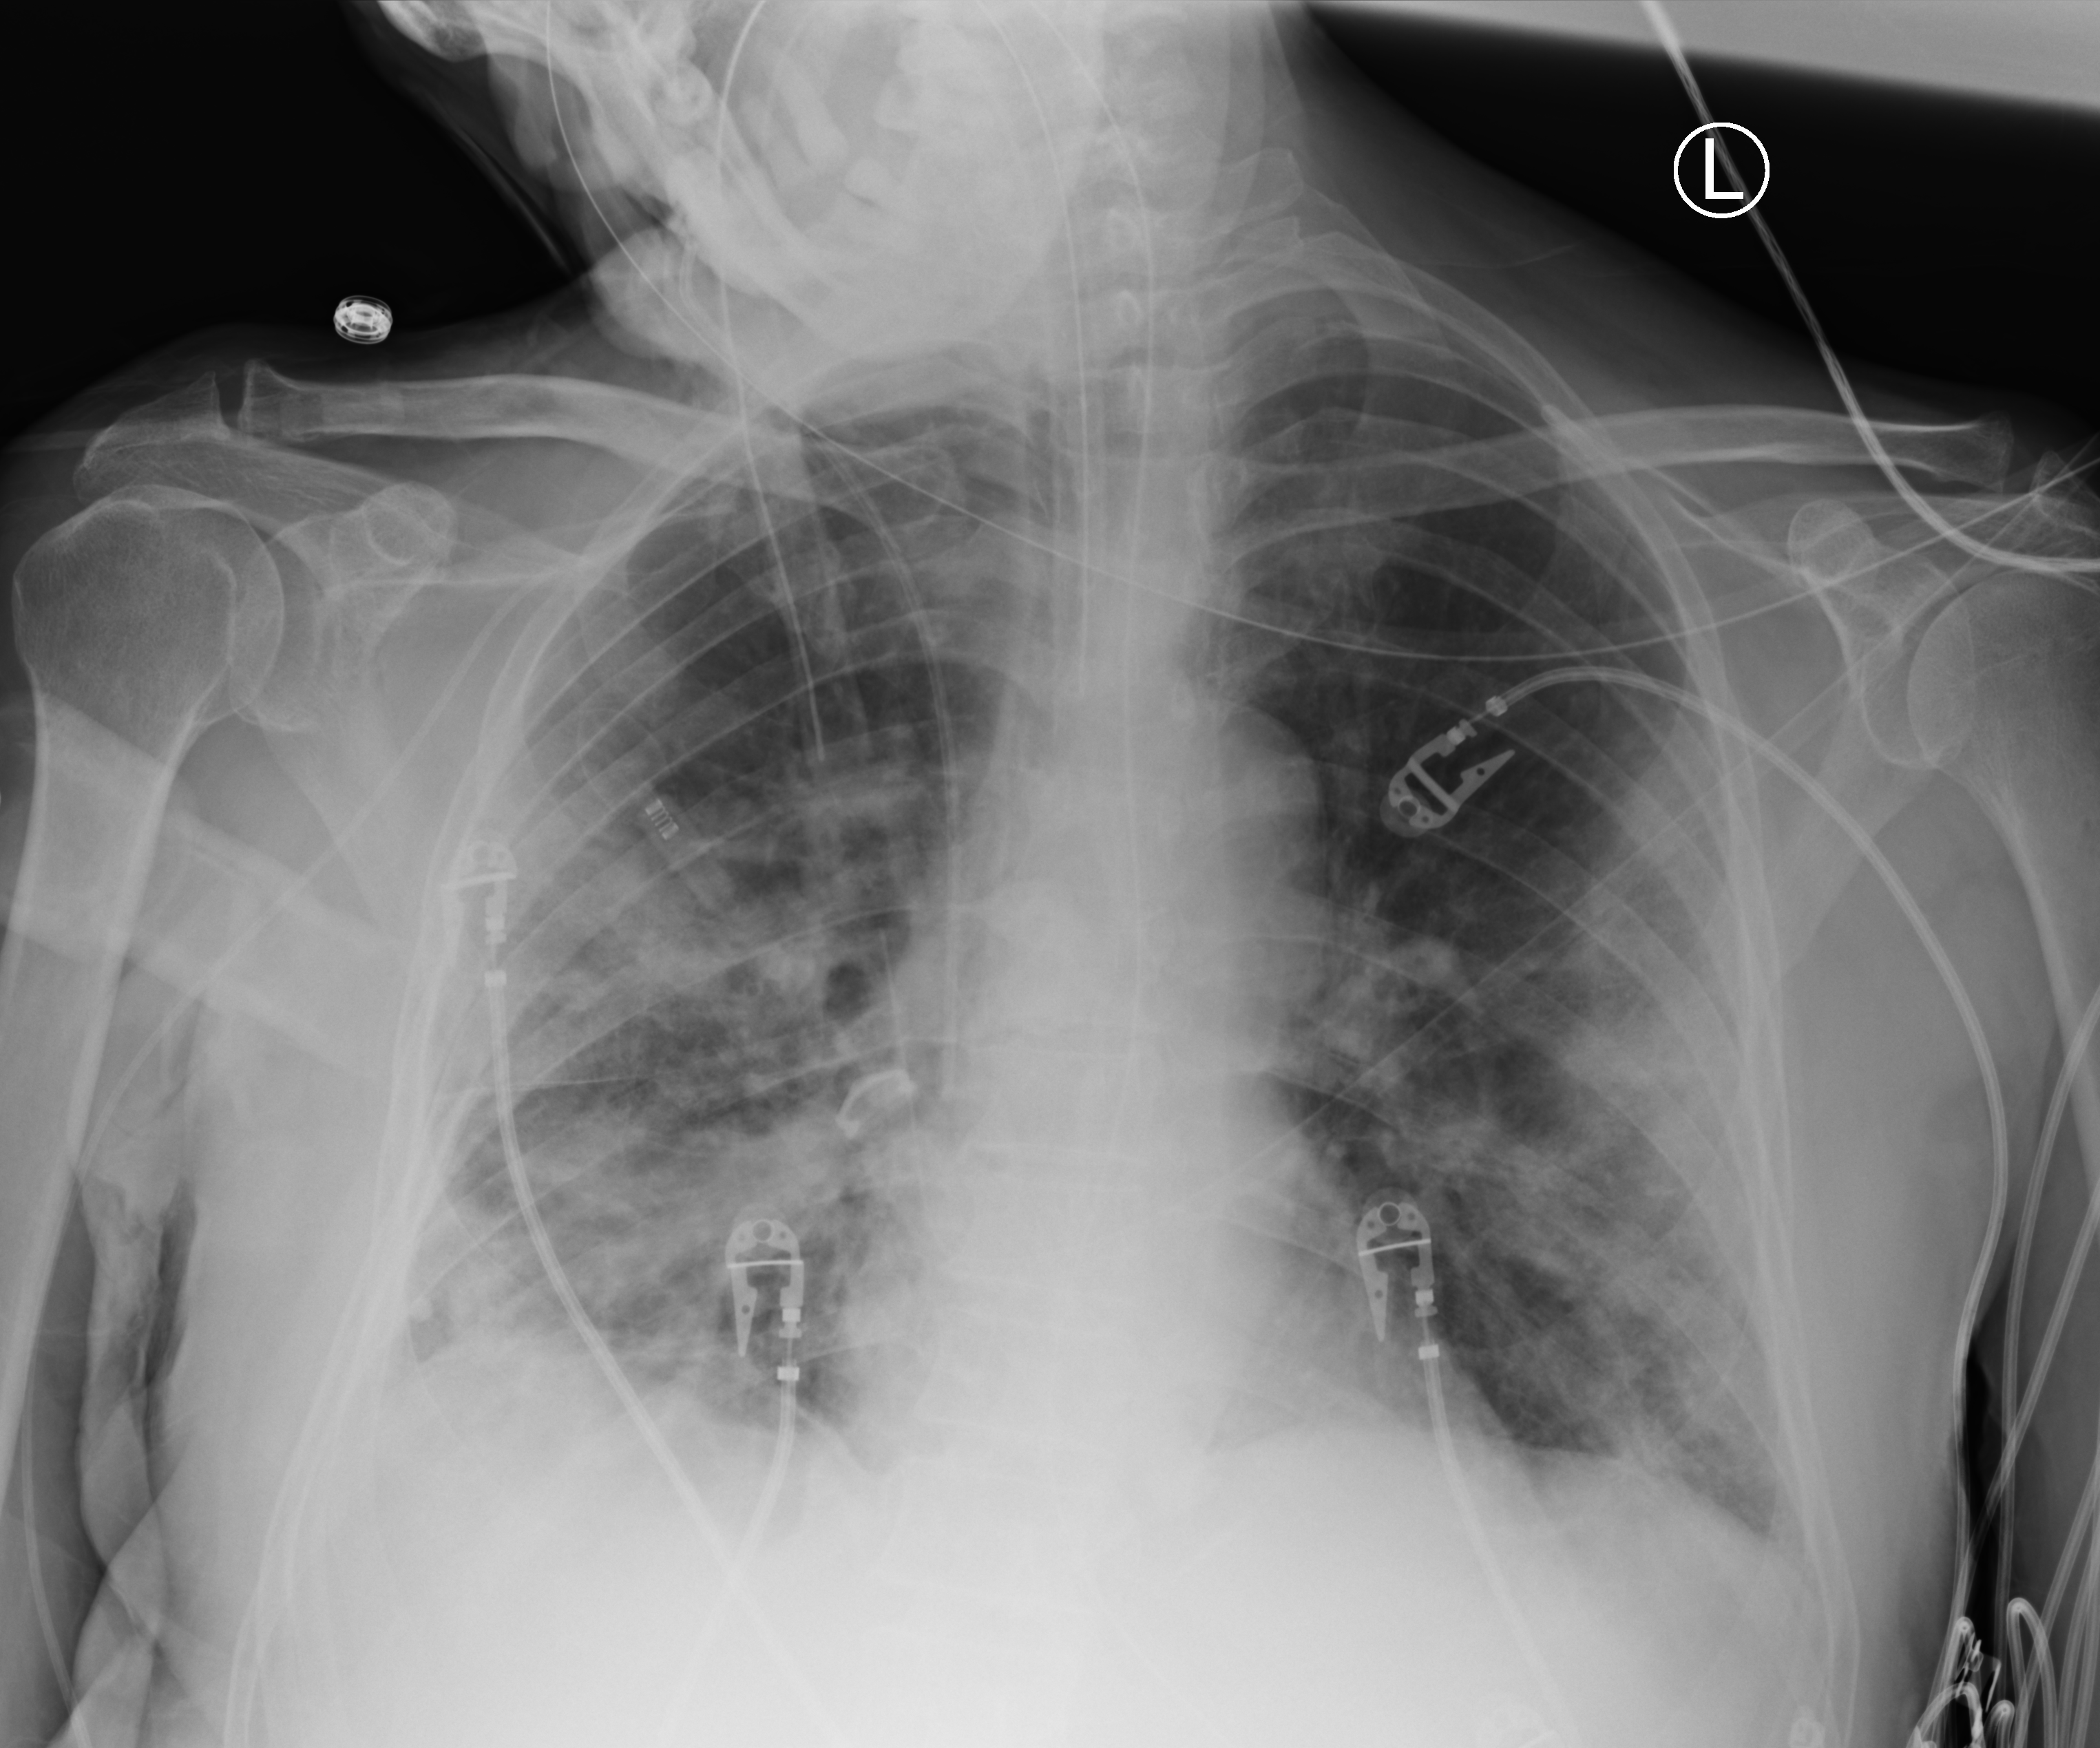
Bedside chest radiograph (computed radiography), anteroposterior (AP) projection. Male patient hospitalised with COVID-19, age 75–90 years.
From the hospital-stay record, not from the radiograph (when in the stay this image was taken is not recorded): COPD (admission record): no; mechanically ventilated during this hospital stay: yes; chronic kidney disease (admission record): no.